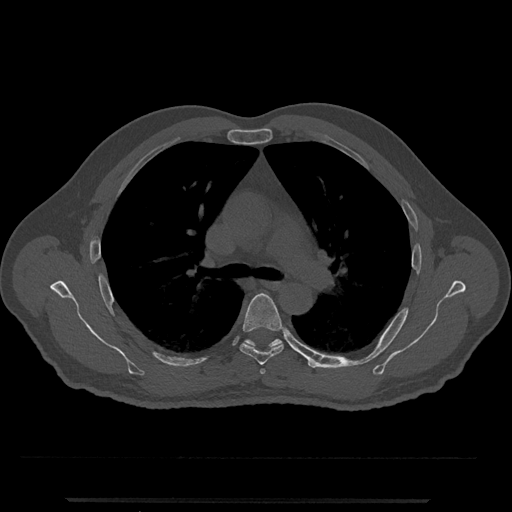
CT including the spine, one axial slice; slice 780 of 797 in the series (ordered by position); reconstruction kernel Br40s/3; 120 kVp; bone window (W 1800 / L 400 HU); 512 × 512 image matrix, field of view 419 × 419 mm. Male patient, age 63 years. From the clinical record (not read from this slice): primary cancer: prostate.
Structures marked on this image (semi-automatically segmented with operator editing):
- T5 vertebra: box from (x=239, y=293) to (x=284, y=365) px
- T6 vertebra: (x=244, y=339)–(x=283, y=348)